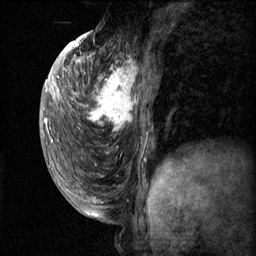
Breast MRI (dynamic contrast-enhanced), one sagittal slice; slice 27 of 60 in the series (ordered by position); dynamic contrast-enhanced series, image 2 of 3 at this slice position (ordered by acquisition); 1.5 T; TE 4.2 ms, TR 11.1 ms; 256 × 256 image matrix, field of view 180 × 180 mm. Female patient, age 50 years.
Annotated regions visible in this slice (semi-automatic segmentation, software-assisted and operator-edited):
- analysis volume of interest (the breast-tissue region the enhancement analysis was run in; not a lesion): bounding box [x1, y1, x2, y2] px = [82, 56, 154, 143]
- tumour enhancement mask (voxels above the 70 % enhancement threshold inside the analysis volume of interest): [82, 56, 148, 143]